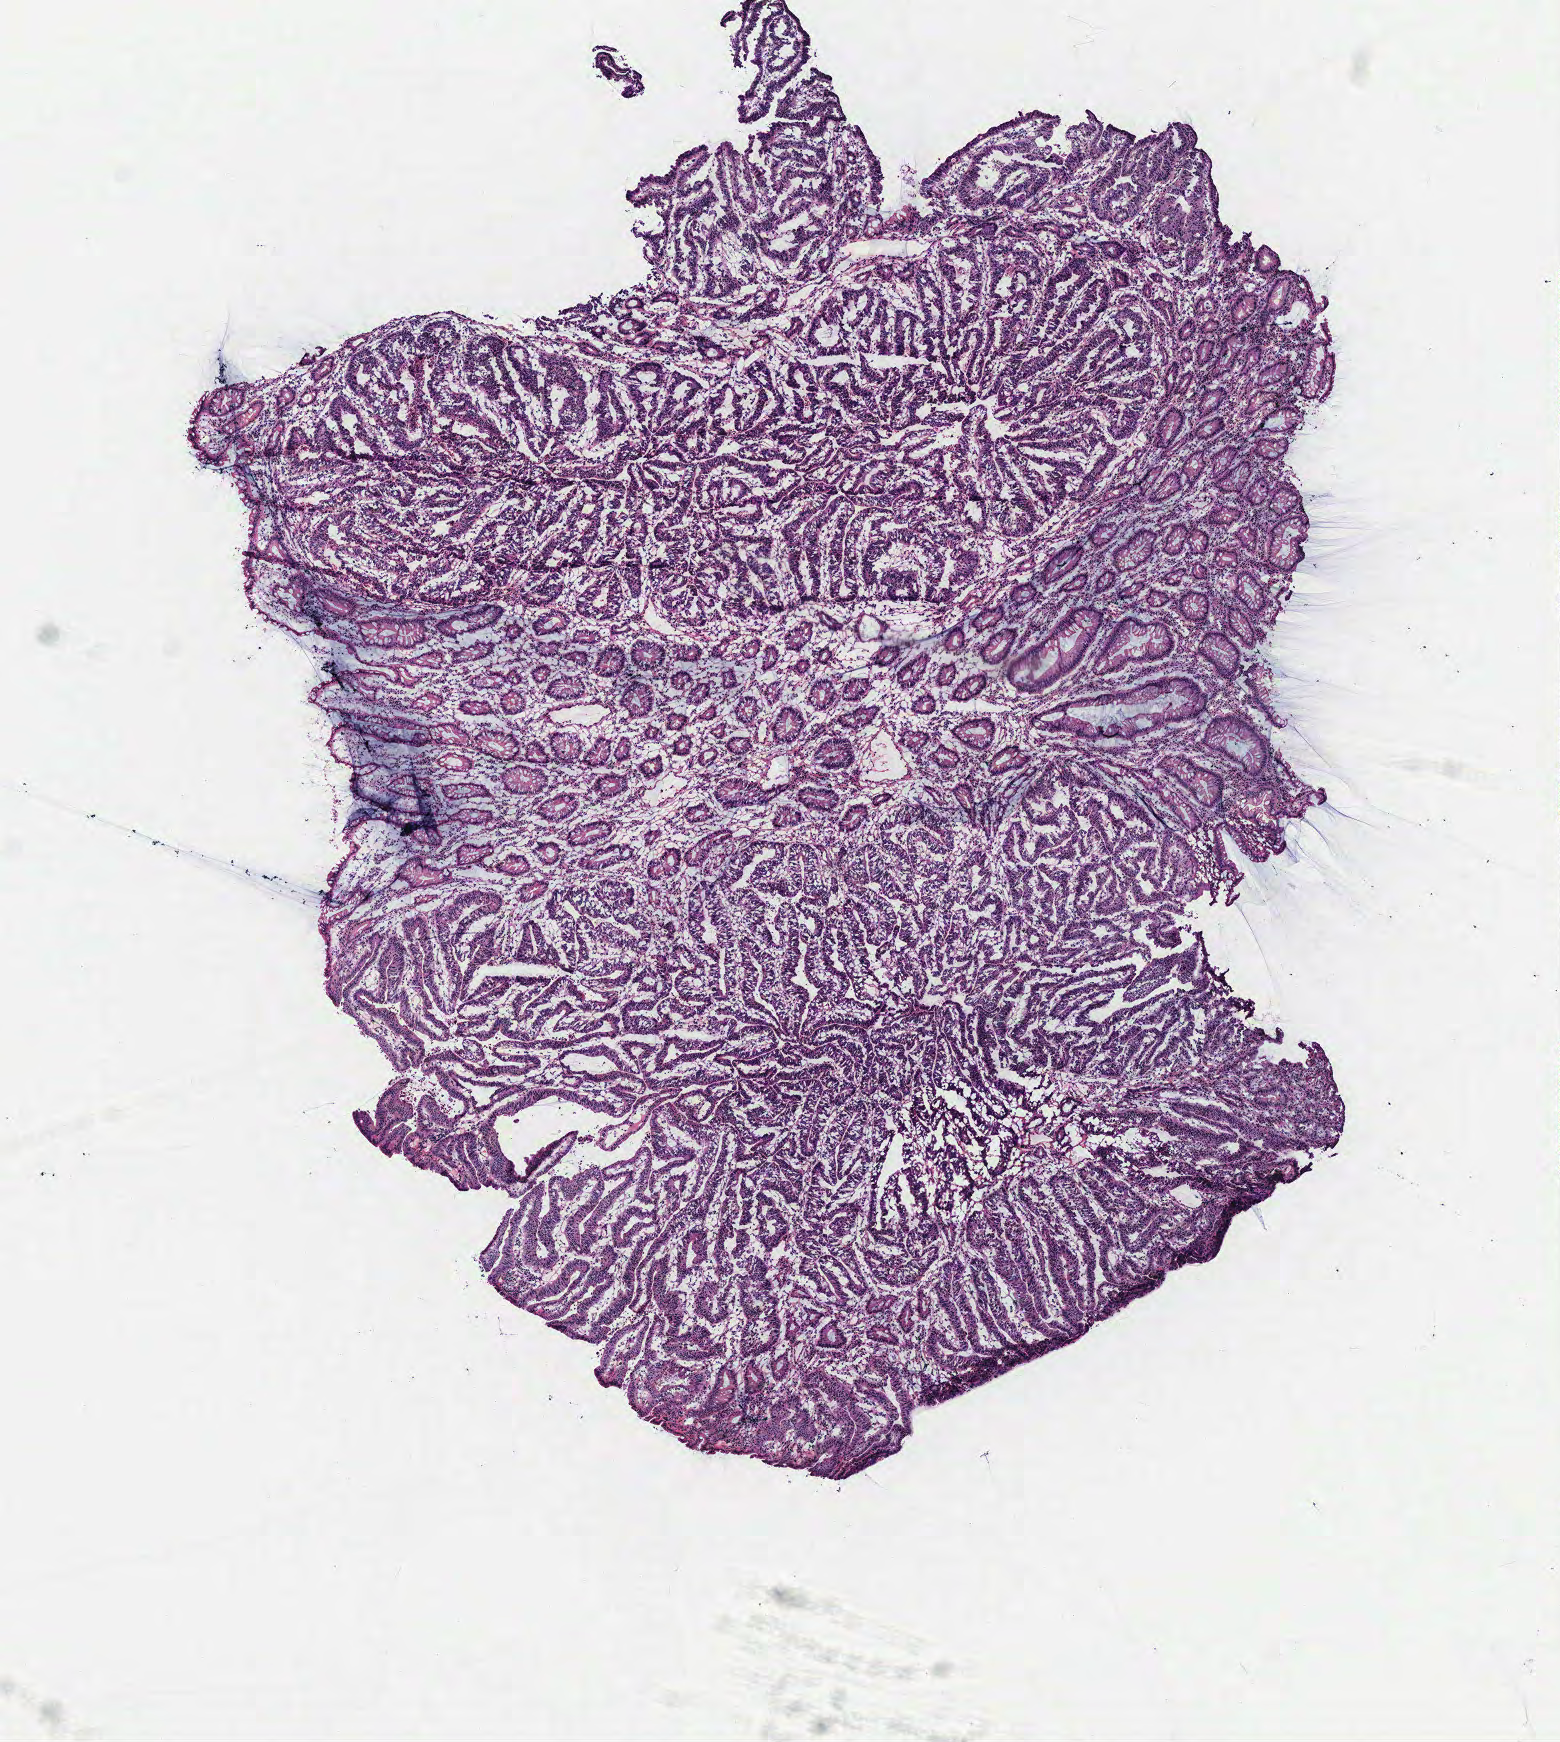
Whole-slide histology image, Hematoxylin and eosin (H&E) stained, shown as a low-resolution overview of the whole scanned area (about 6.2 x 7.0 mm). Colon, normal (non-tumour) tissue. 51-year-old male patient.
This section: normal (non-tumour) tissue from the same patient. Patient diagnosis: Adenocarcinoma, NOS.